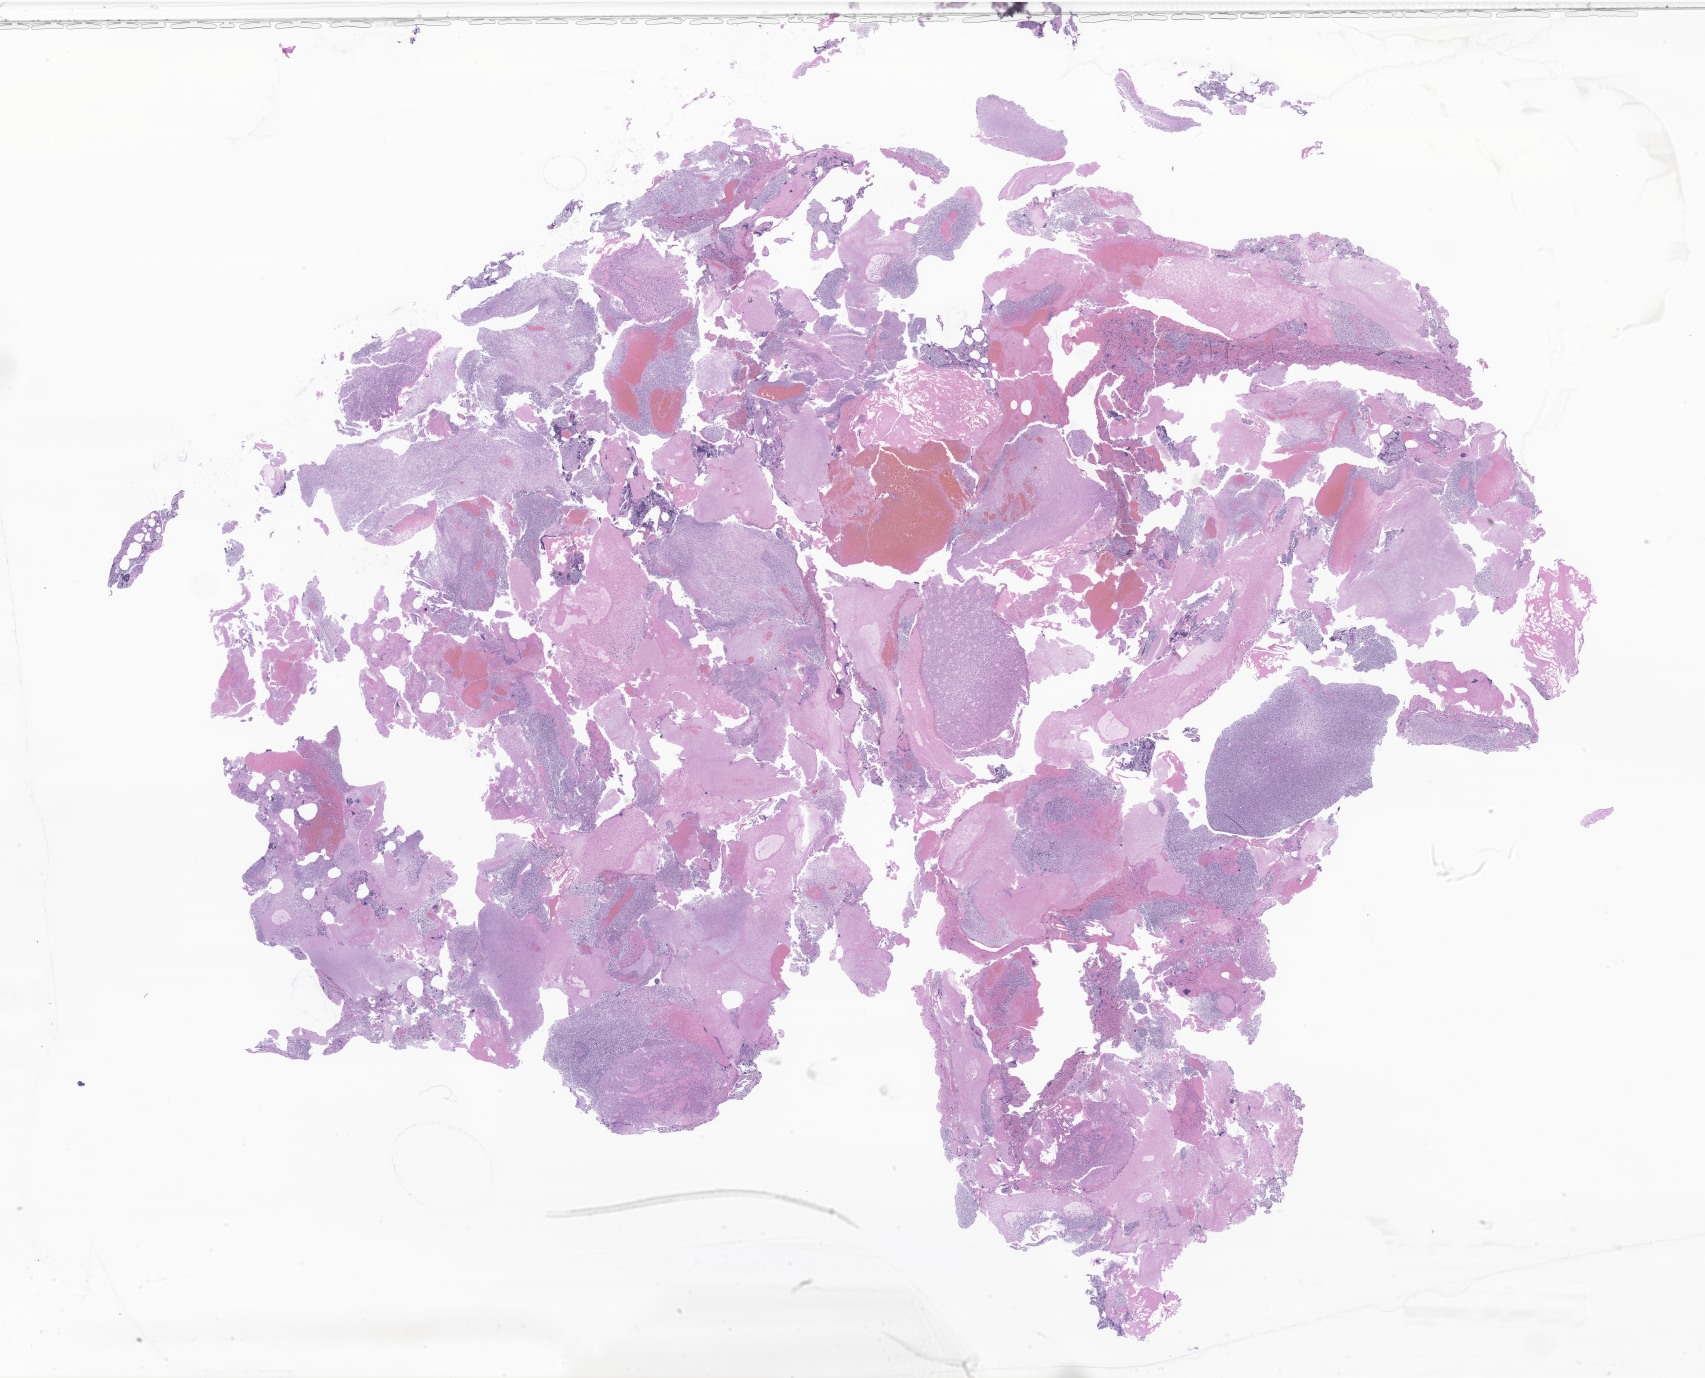
Digitized haematoxylin and eosin-stained section of tumor tissue from the brain — a low-resolution overview of the entire scanned area, about 28.8 x 23.2 mm; FFPE section. Patient female; age 159 months (13 years 3 months).
• recorded diagnosis: Sarcoma, NOS